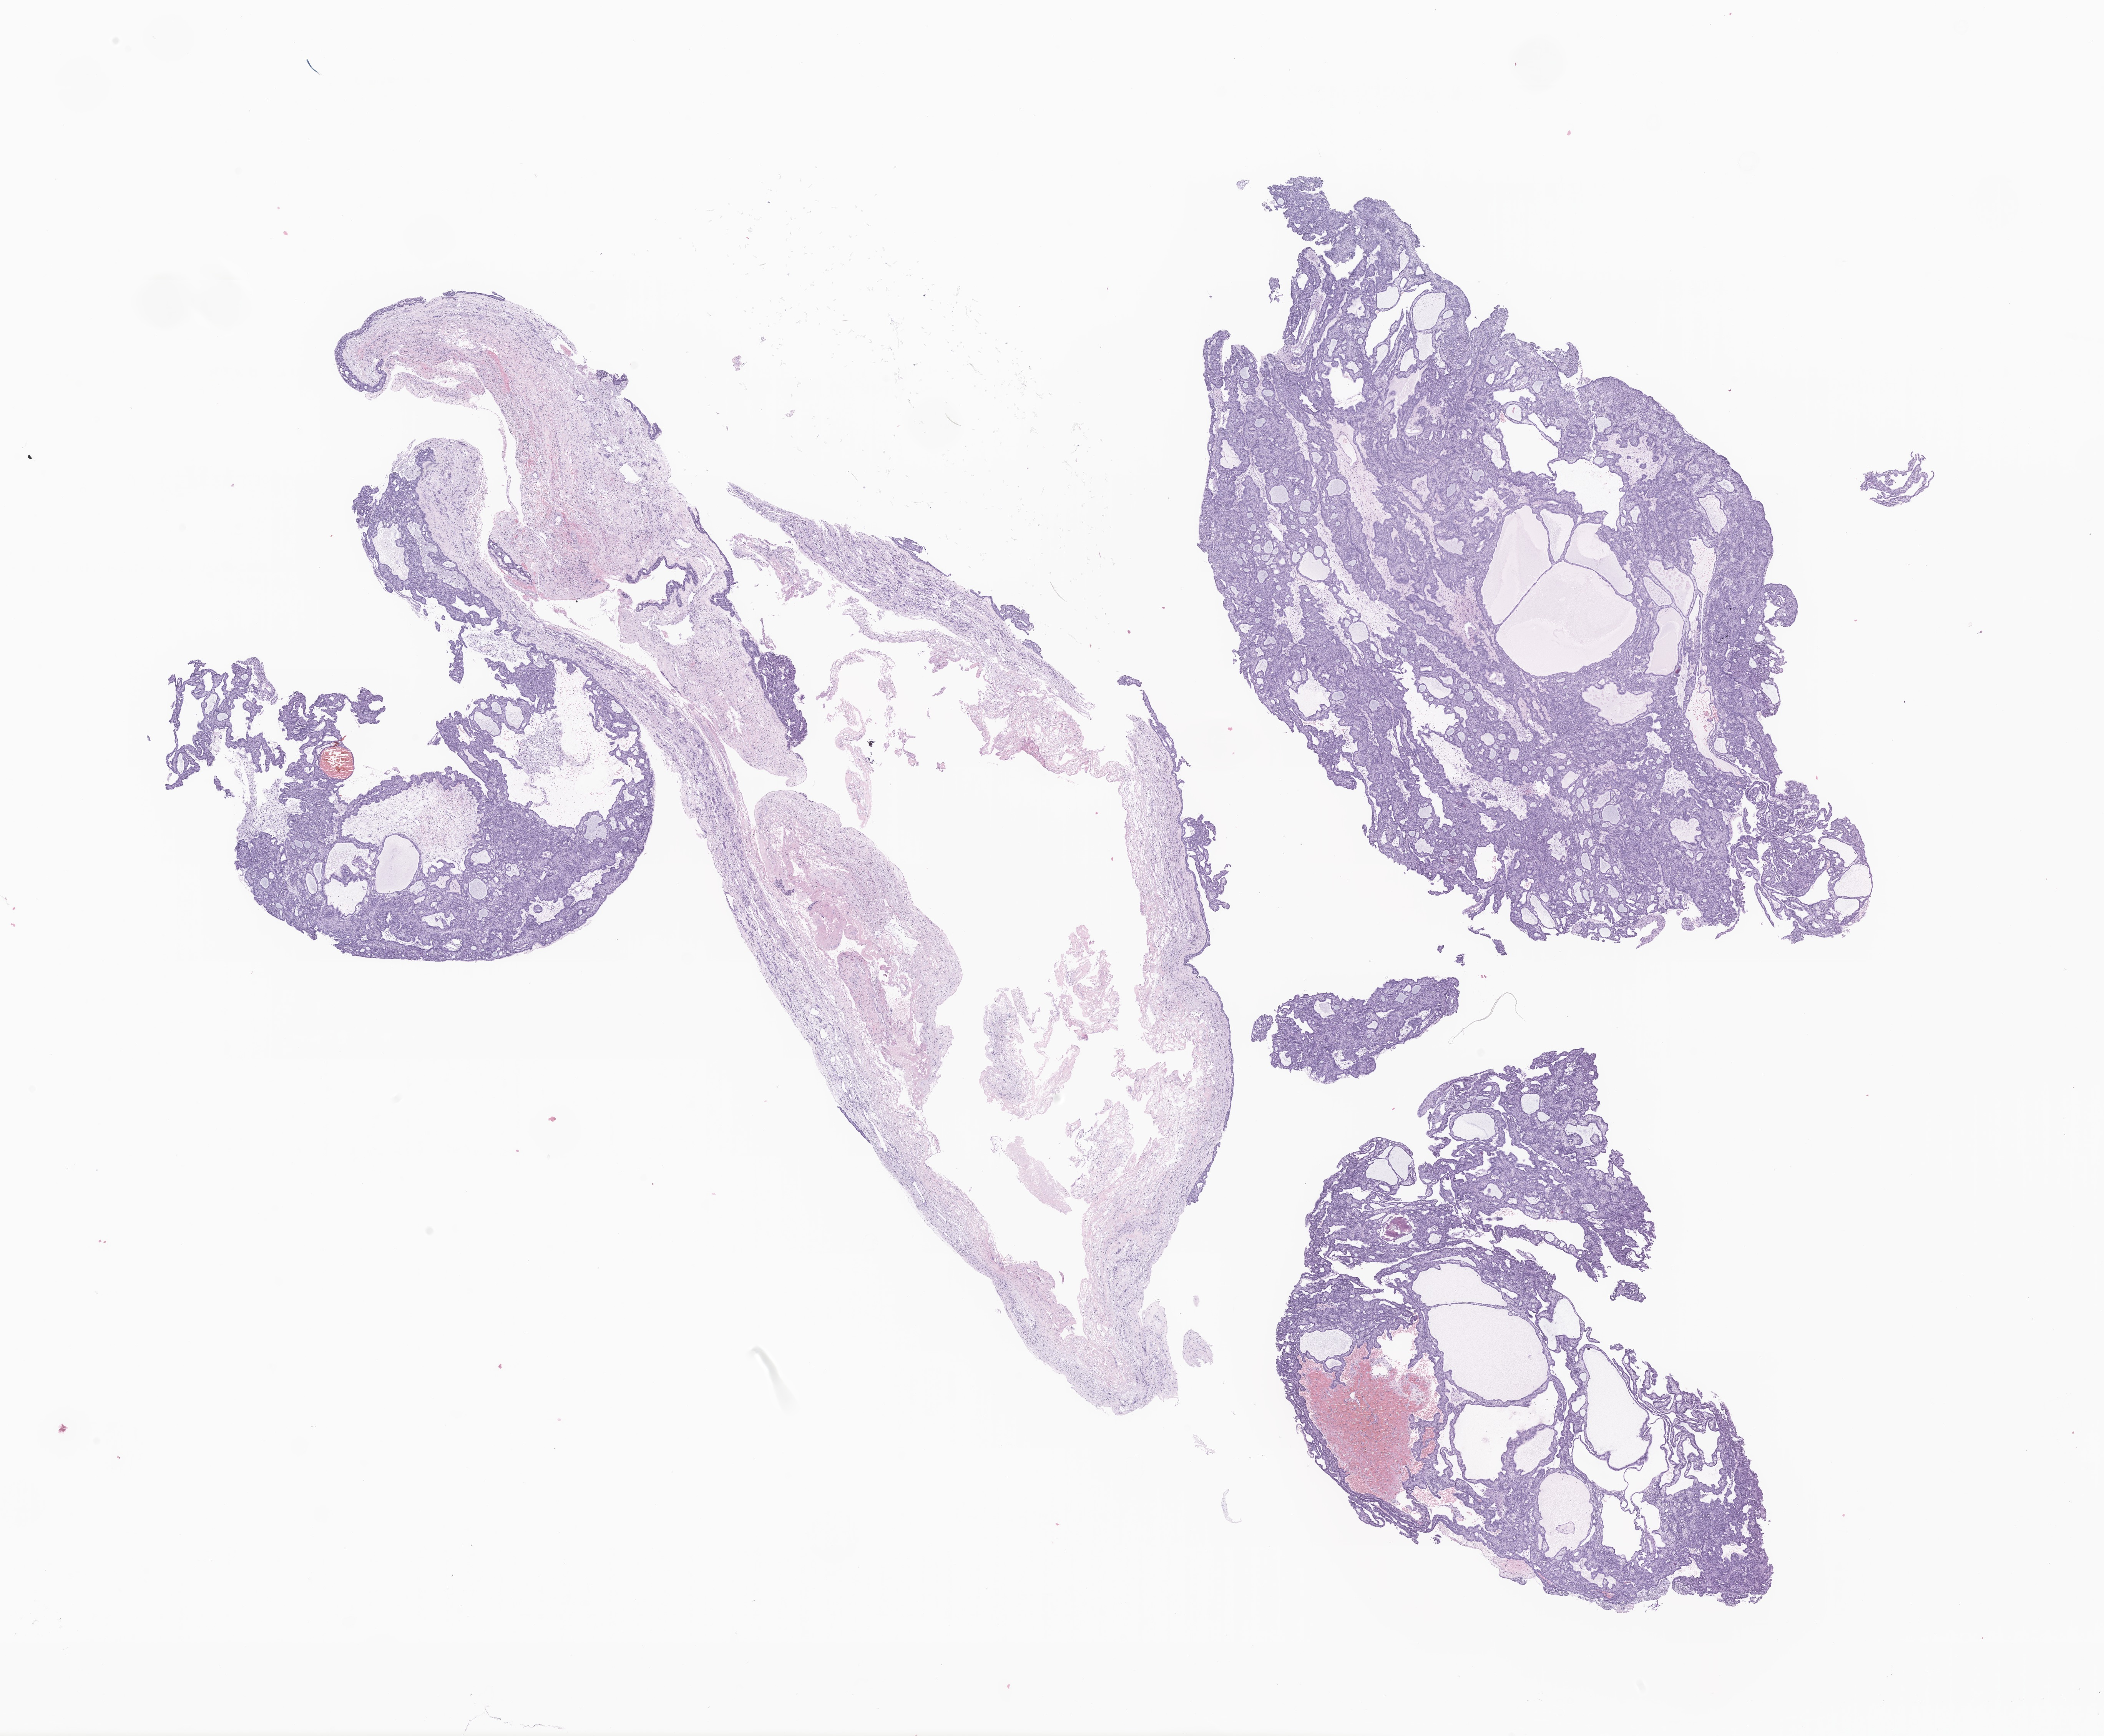
Digitized H&E-stained section of tumor tissue from the brain — shown as a low-resolution overview of the whole scanned area (about 23.1 x 19.0 mm); formalin-fixed, paraffin-embedded (FFPE) tissue. Patient female; age 147 months (12 years 3 months).
• recorded diagnosis: Craniopharyngioma, adamantinomatous